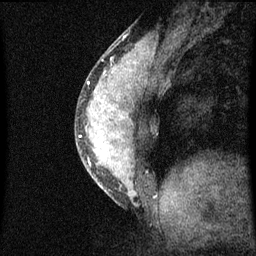
Breast MRI (dynamic contrast-enhanced), one sagittal slice. Slice 23 of 60 in the series (ordered by position). Dynamic contrast-enhanced series, image 2 of 3 at this slice position (ordered by acquisition). 1.5 T. TE 4.2 ms, TR 8 ms. 2 mm slice thickness. 256 × 256 image matrix. Female patient, age 33 years.
Annotated regions visible in this slice (semi-automatically segmented with operator editing):
- analysis volume of interest (the breast-tissue region the enhancement analysis was run in; not a lesion): bounding box [x1, y1, x2, y2] px = [75, 56, 154, 205]
- tumour enhancement mask (voxels above the 70 % enhancement threshold inside the analysis volume of interest): [80, 62, 137, 165]